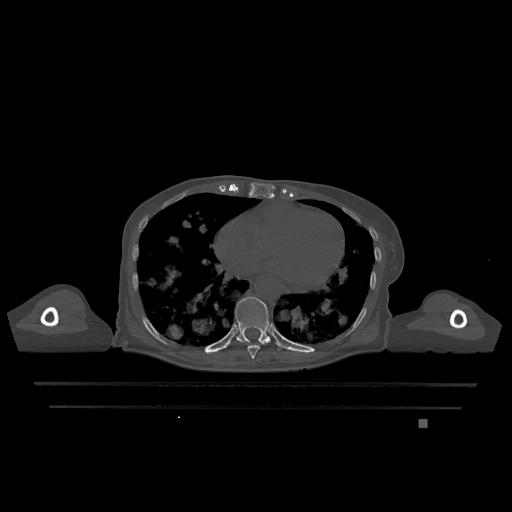
CT including the spine, one axial slice. Position 665 of 1317 along the scan axis. Bone window (W 1800 / L 400 HU). 0.5 mm slice thickness. 512 × 512 image matrix, field of view 500 × 500 mm. Patient: female, 74 years. Case-level facts recorded for this patient, not image findings: primary cancer: lung.
Outlined on this slice (semi-automatically segmented with operator editing):
- T10 vertebra: bounding box <235,297,279,350> (left, top, right, bottom; pixels)
- T9 vertebra: <242,341,265,359>